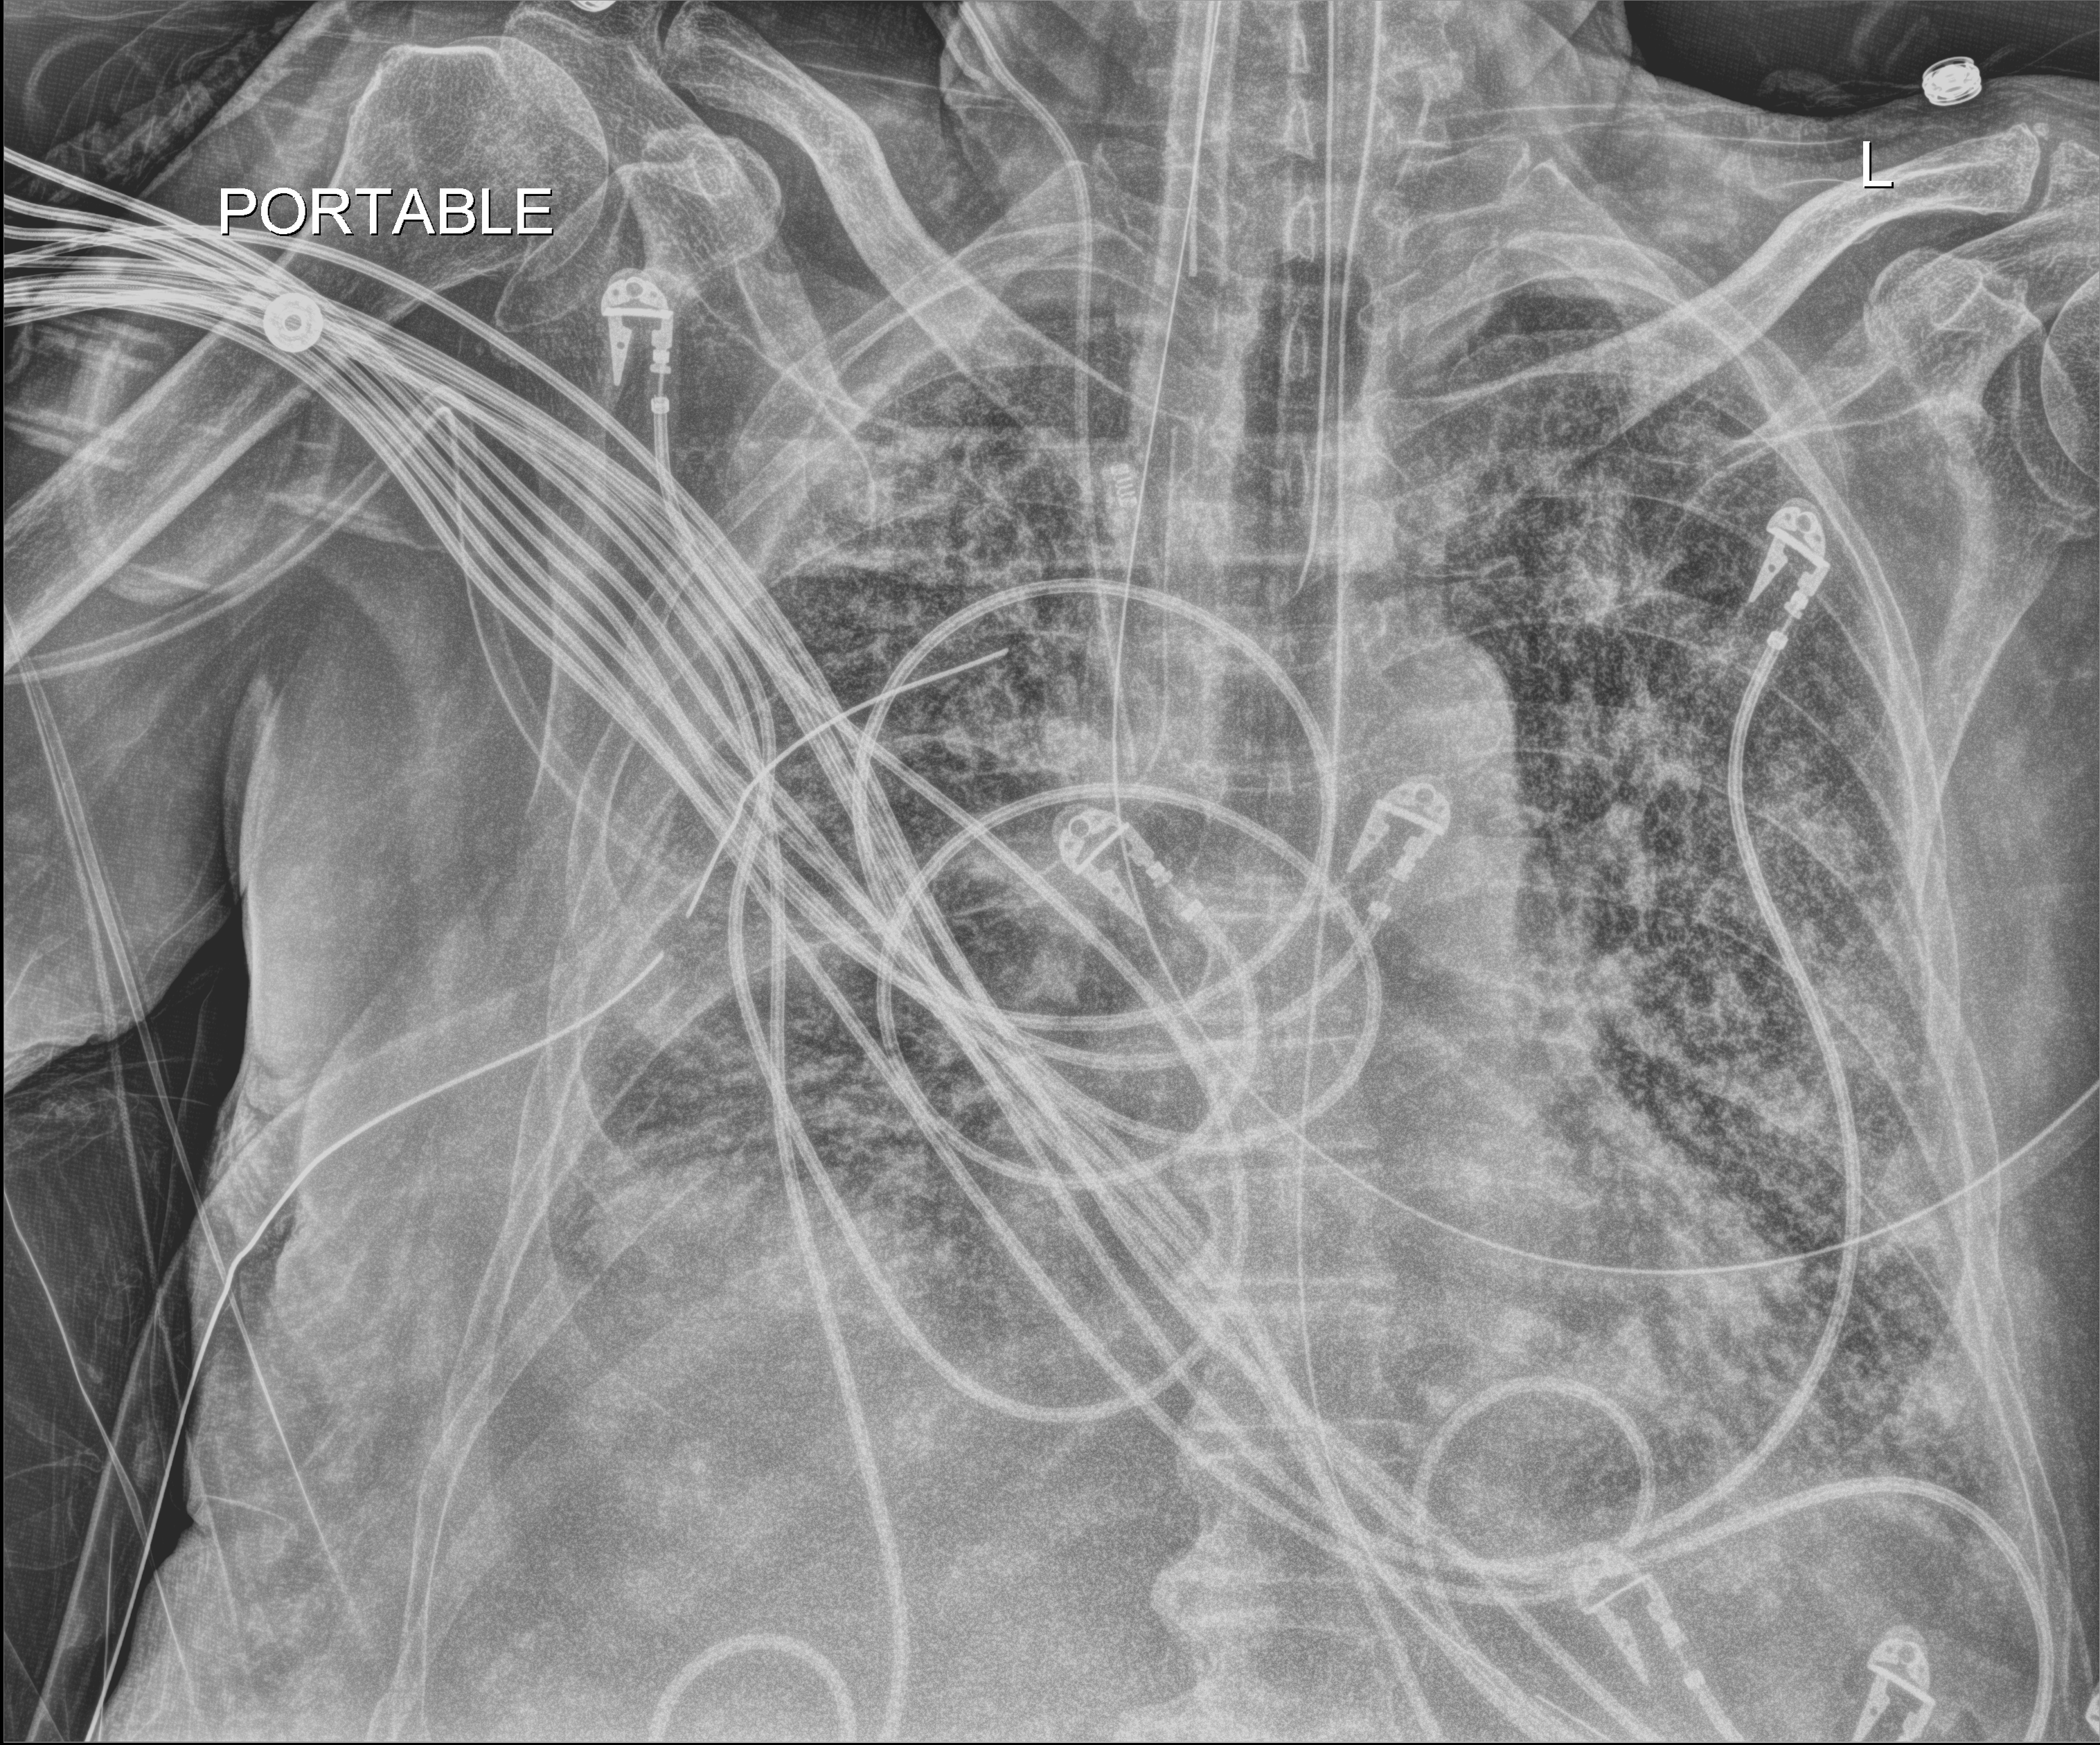
Bedside chest radiograph (digital radiography); anteroposterior (AP) projection. Patient hospitalised with COVID-19; male, aged 75–90 years.
From the hospital-stay record, not from the radiograph (when in the stay this image was taken is not recorded): diabetes (admission record): no; mechanically ventilated during this hospital stay: yes; admitted to intensive care during this hospital stay: yes.